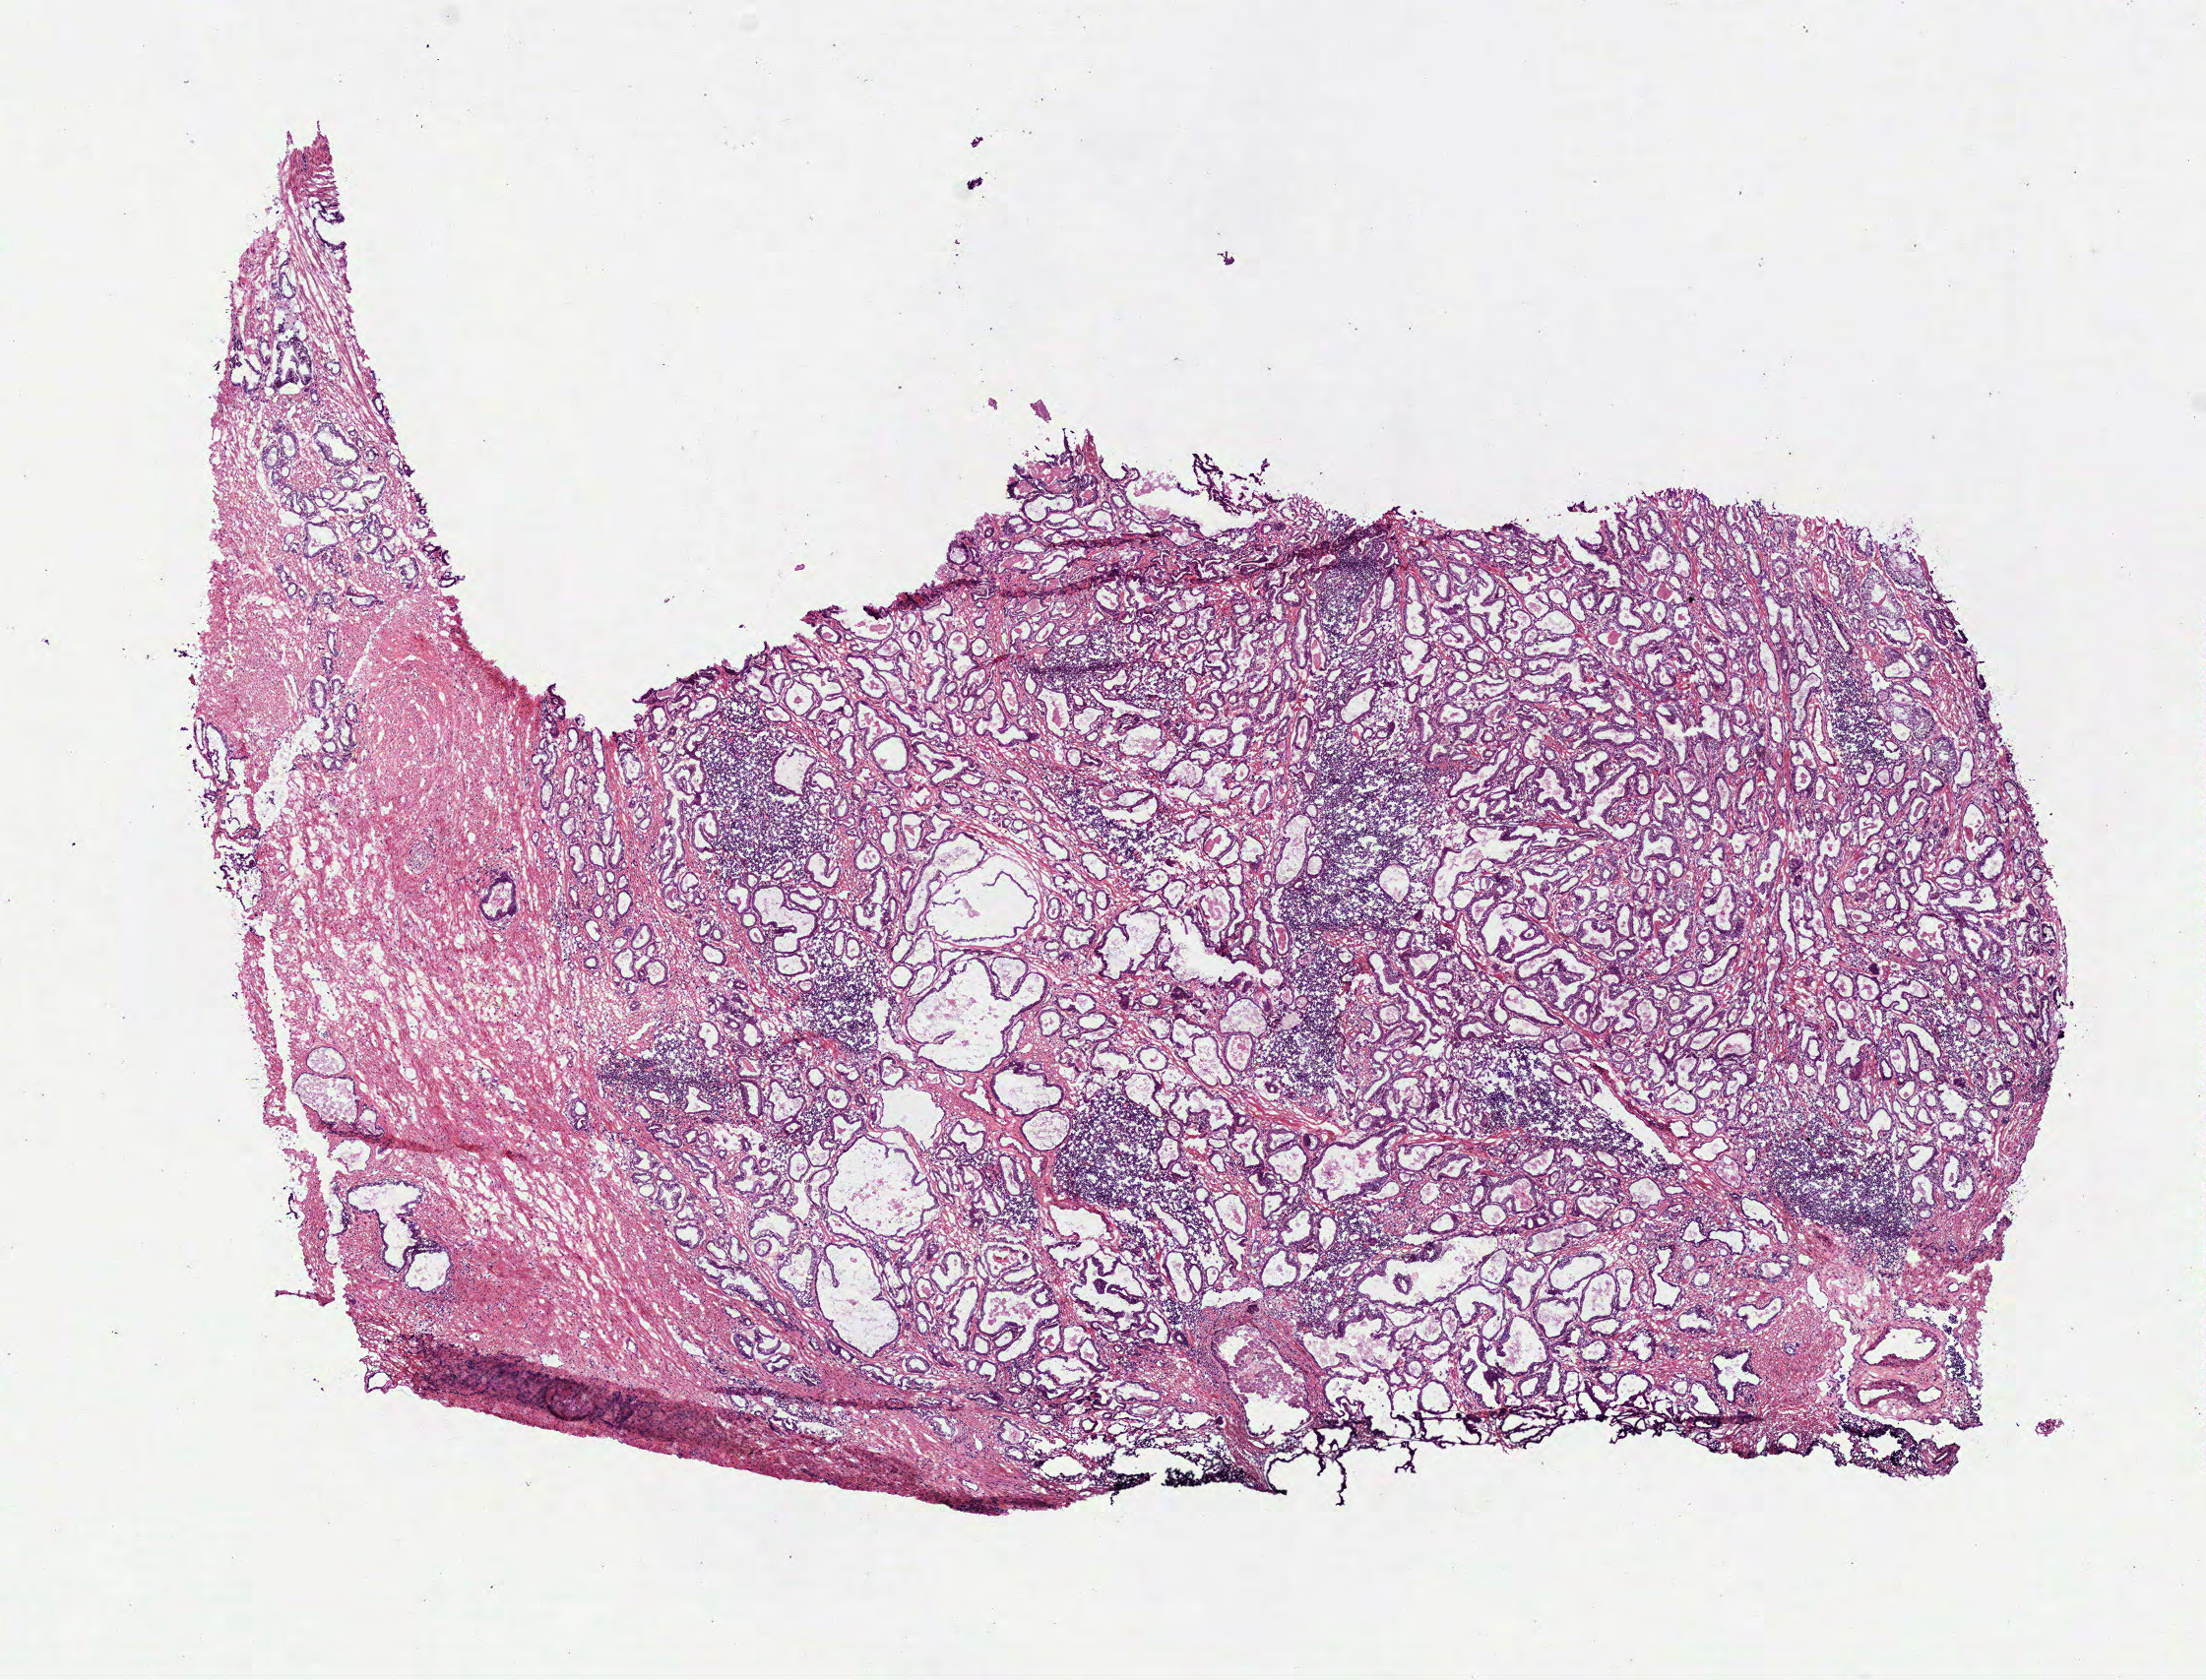
Digitized H&E tissue section (whole slide) — low-resolution overview of the scanned area, about 9.0 x 6.9 mm (from a 40x scan). Frozen section. Prostate, primary tumour sample. Male patient; age at initial diagnosis 61 years. Gleason score: 6 (3+3). Composition of this section per pathologist review: tumour cells 65%, tumour nuclei 75%, normal cells 20%, stromal cells 15%, necrosis 0%. Inflammatory infiltration, as recorded: lymphocyte infiltration 15%, monocyte infiltration 0%, neutrophil infiltration 0%.
Diagnosis: Acinar cell carcinoma (prostate gland). Laterality: bilateral.